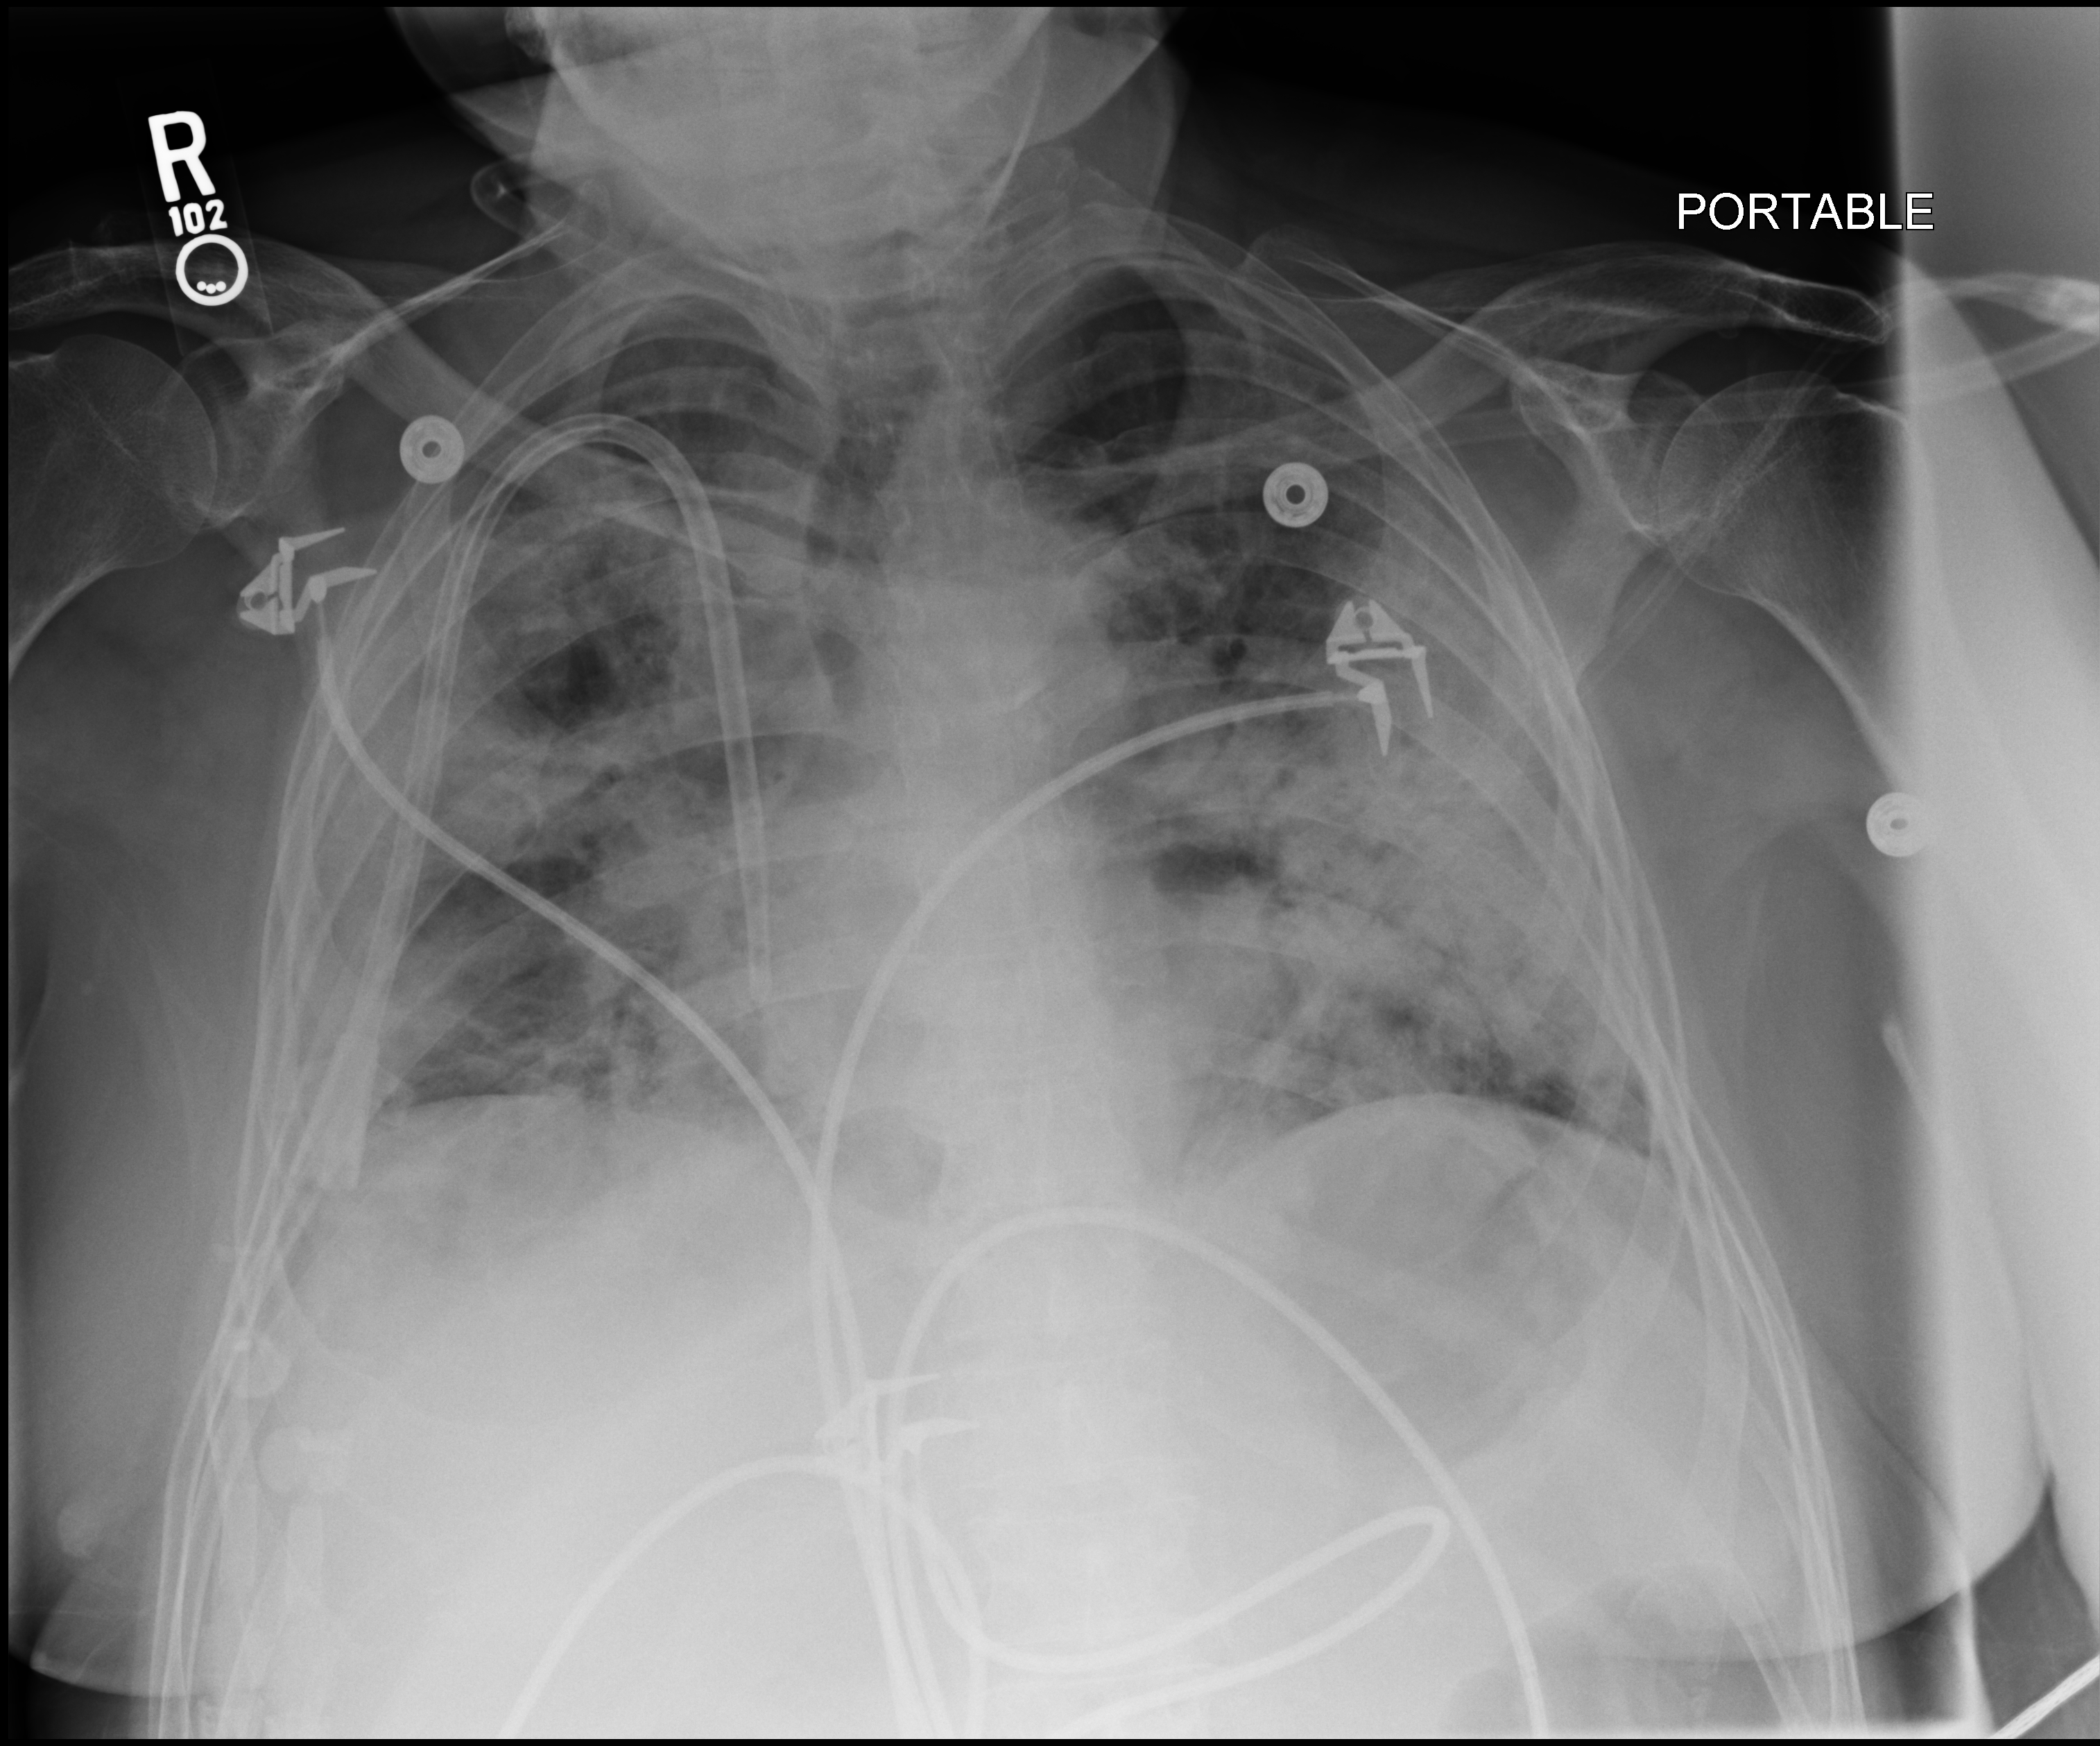
Portable chest radiograph; anteroposterior (AP) projection. Patient hospitalised with COVID-19; male, aged 60–74 years.
From the hospital-stay record, not from the radiograph (when in the stay this image was taken is not recorded): mechanically ventilated during this hospital stay: no.